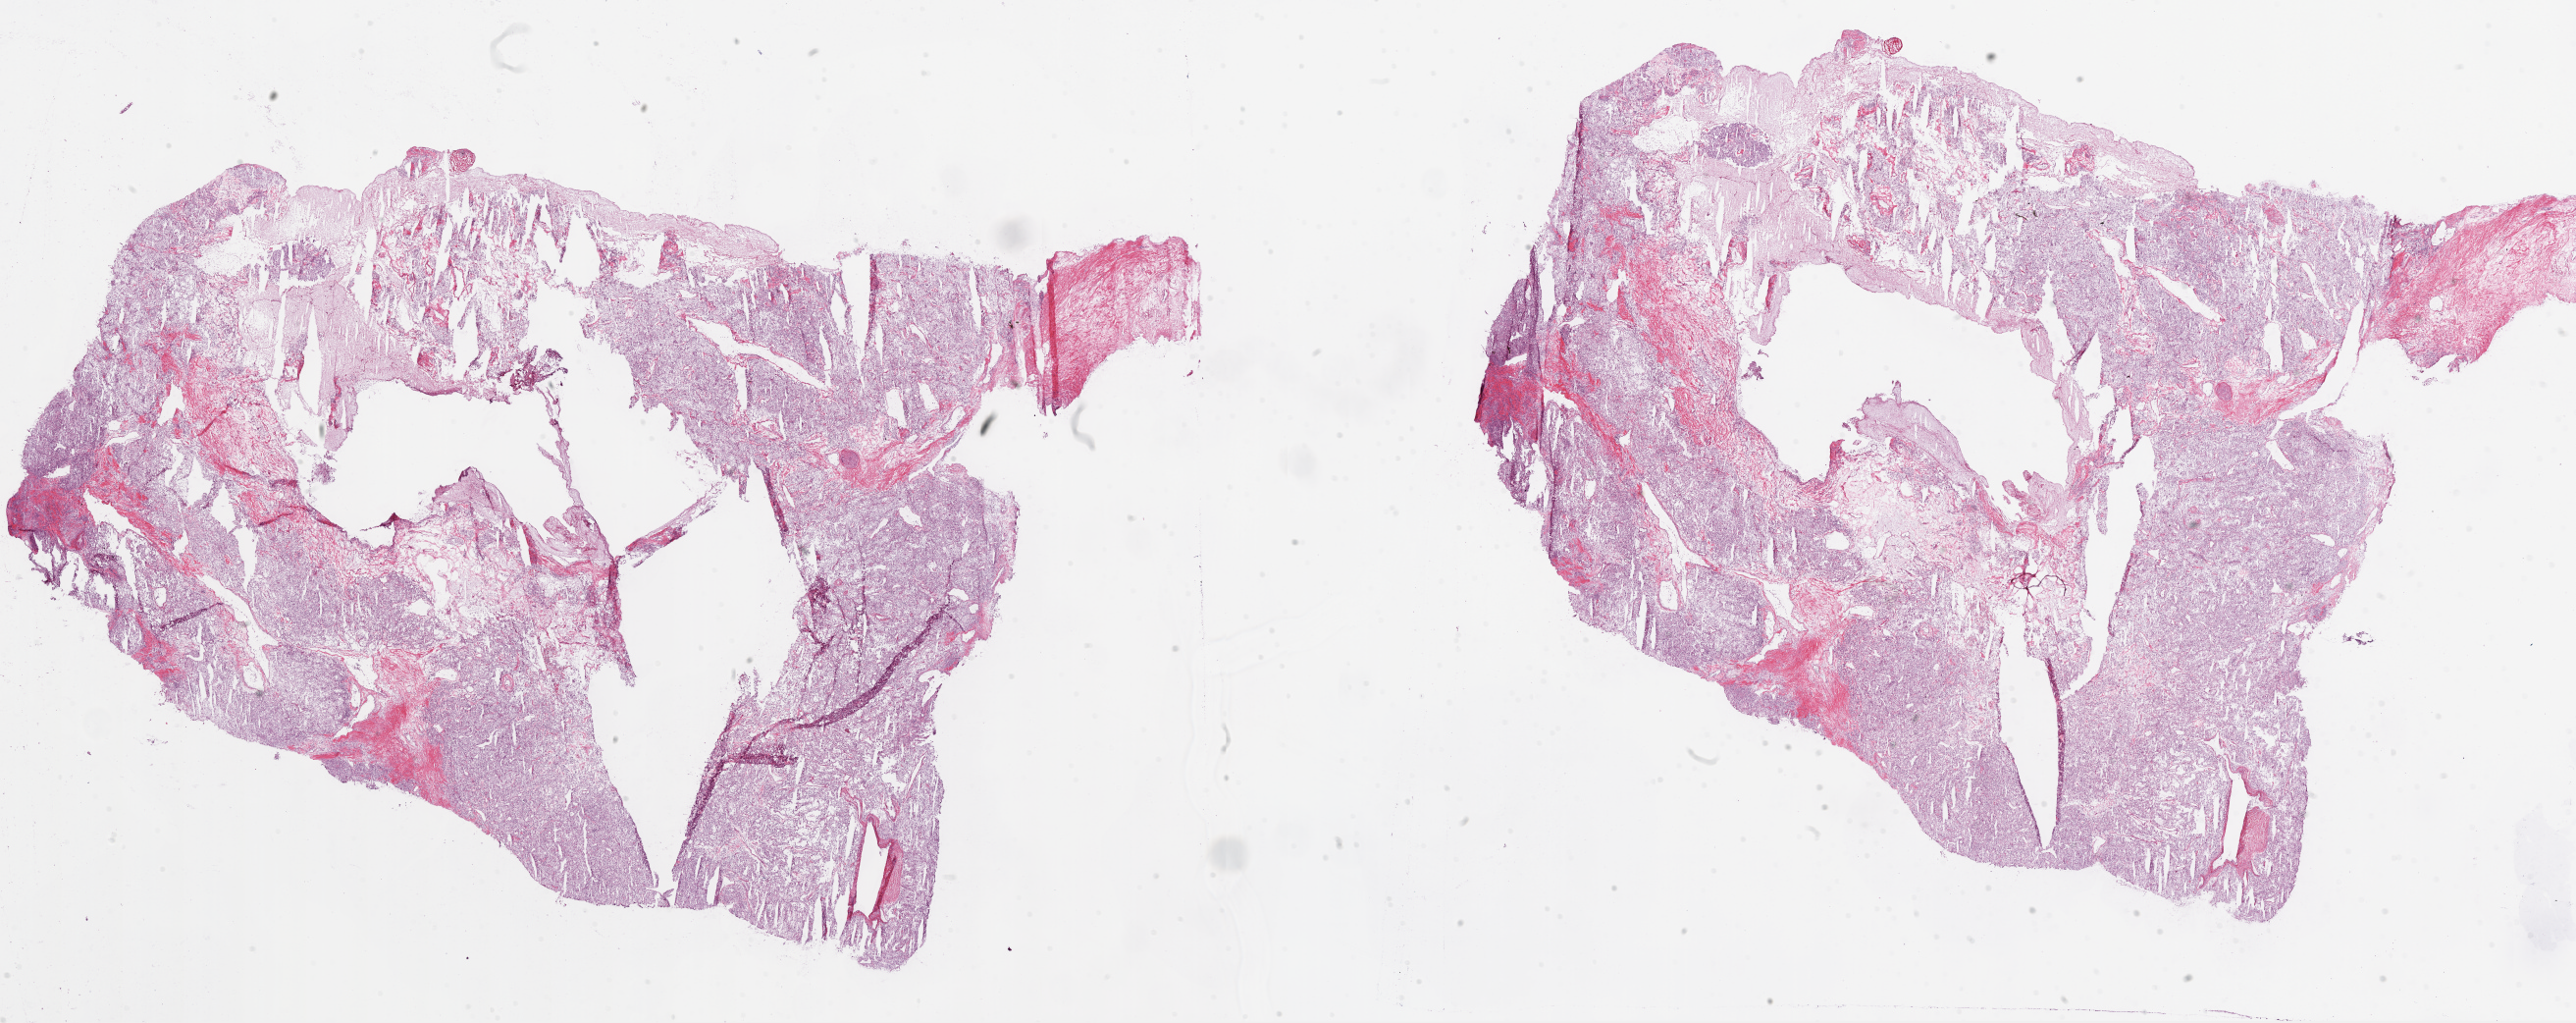
Digitized Hematoxylin and eosin (H&E) stained tissue section (whole slide) — a low-resolution overview of the entire scanned area, about 42.1 x 16.7 mm. Frozen section. Primary tumour sample from the kidney. Male patient; age at initial diagnosis 64 years. Histologic grade: G2 (moderately differentiated). Pathologist review of this section (percent, as recorded): tumour cells 80%, tumour nuclei 80%, normal cells 0%, stromal cells 20%, necrosis 0%.
AJCC pathologic stage: I. Laterality: right. Pathologic diagnosis: Clear cell adenocarcinoma, NOS.